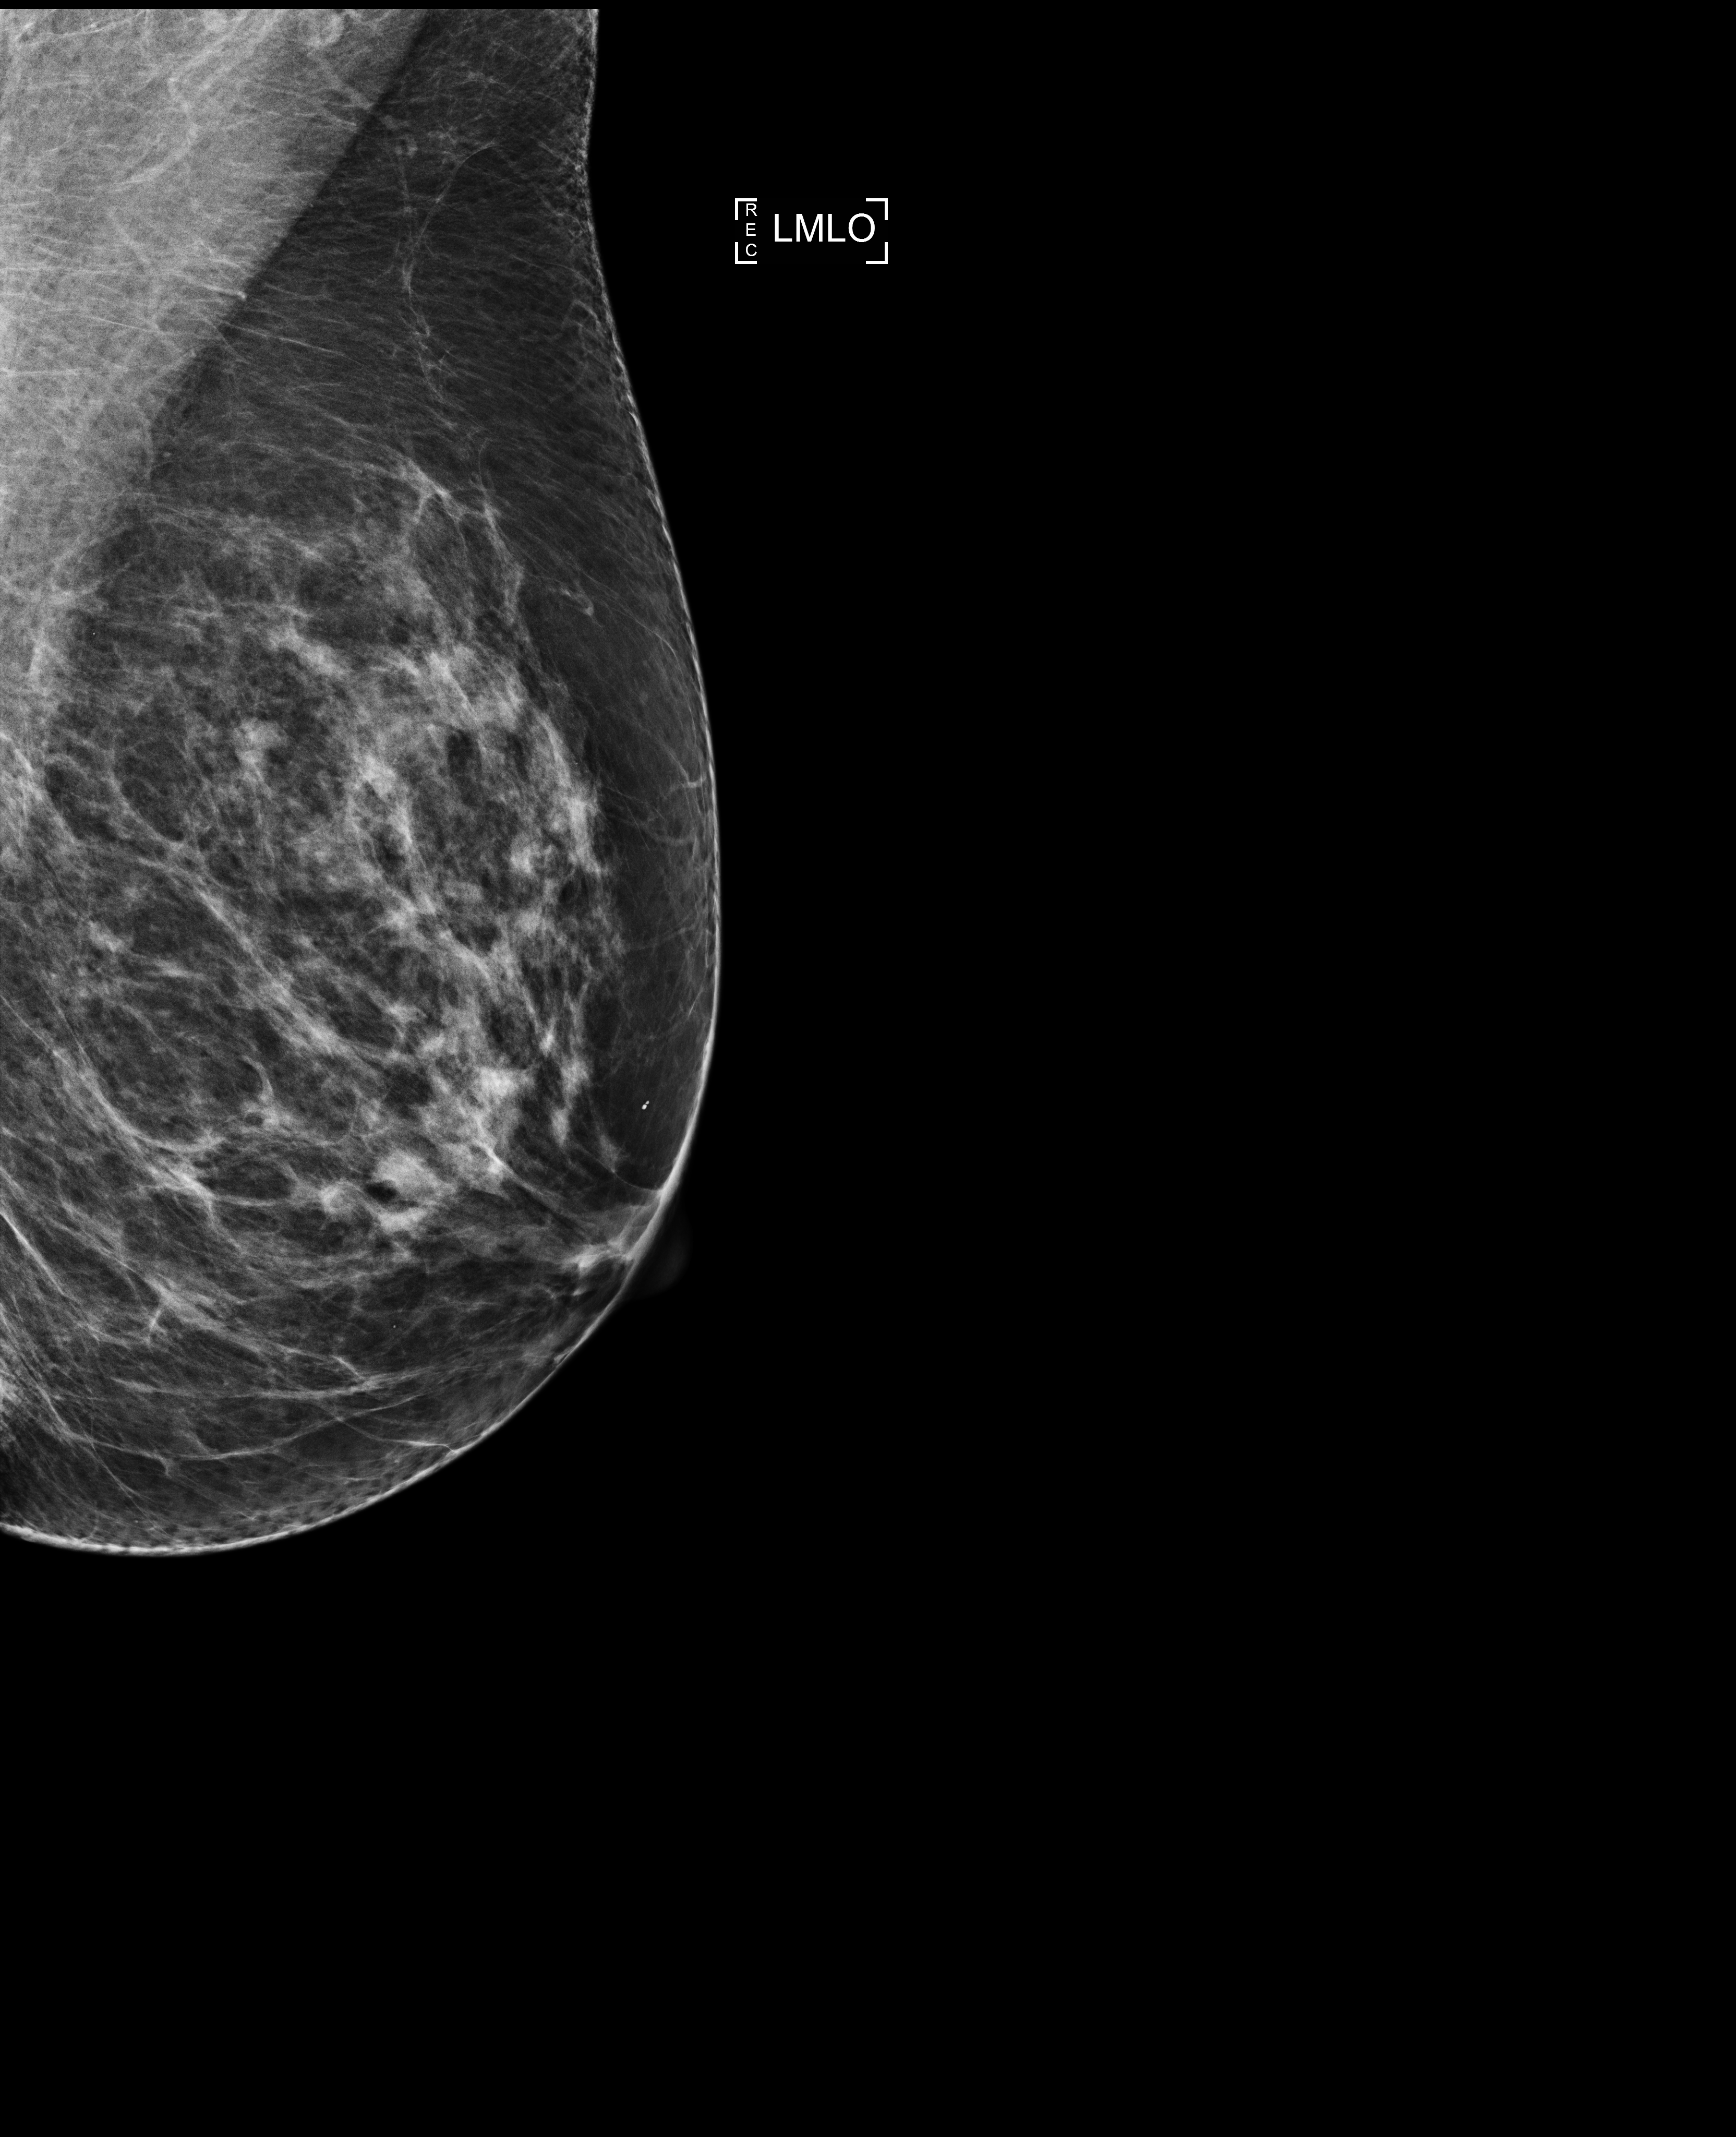
Screening examination; compressed breast thickness 74 mm. Patient aged 53 years (female).
Image type: full-field digital mammogram. Breast: left. Projection: medio-lateral oblique projection.